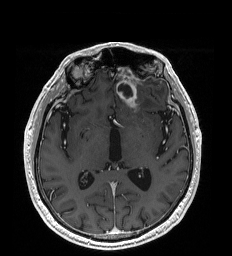
Brain MRI from a brain-tumour surgery series, one axial slice. Slice 106 of 192 in the series (ordered by position). T1-weighted post-contrast. 232 × 256 image matrix. Case-level facts recorded for this patient, not image findings: histopathology: Glioblastoma; WHO grade: 4; IDH mutation: no.
Structures marked on this image (outlined manually by an expert reader):
- tumour: box from (x=118, y=85) to (x=137, y=108) px